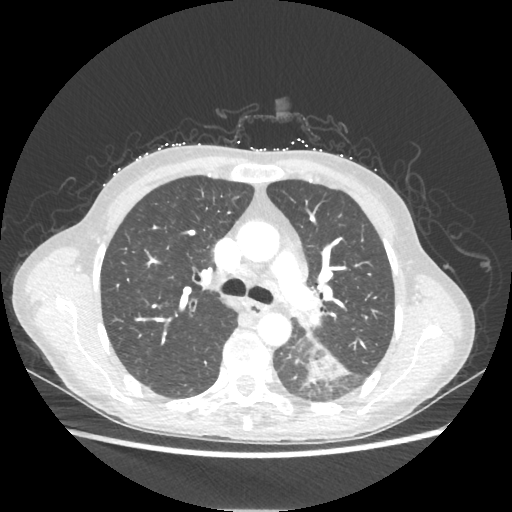
Chest CT, one axial slice; slice 141 of 221 in the series (ordered by position); reconstruction kernel STANDARD; 80 kVp; lung window (W 1500 / L -600 HU); 1.25 mm slice thickness; 512 × 512 image matrix, field of view 360 × 360 mm. Patient: female, 53 years. From the clinical record (not read from this slice): clinical TNM (as recorded): T3 N0 M0.
Outlined on this slice (rectangle marked by the reading radiologist):
- lung tumour (recorded histology: adenocarcinoma): bounding box (x1, y1, x2, y2) in pixels: (305, 353, 347, 384)